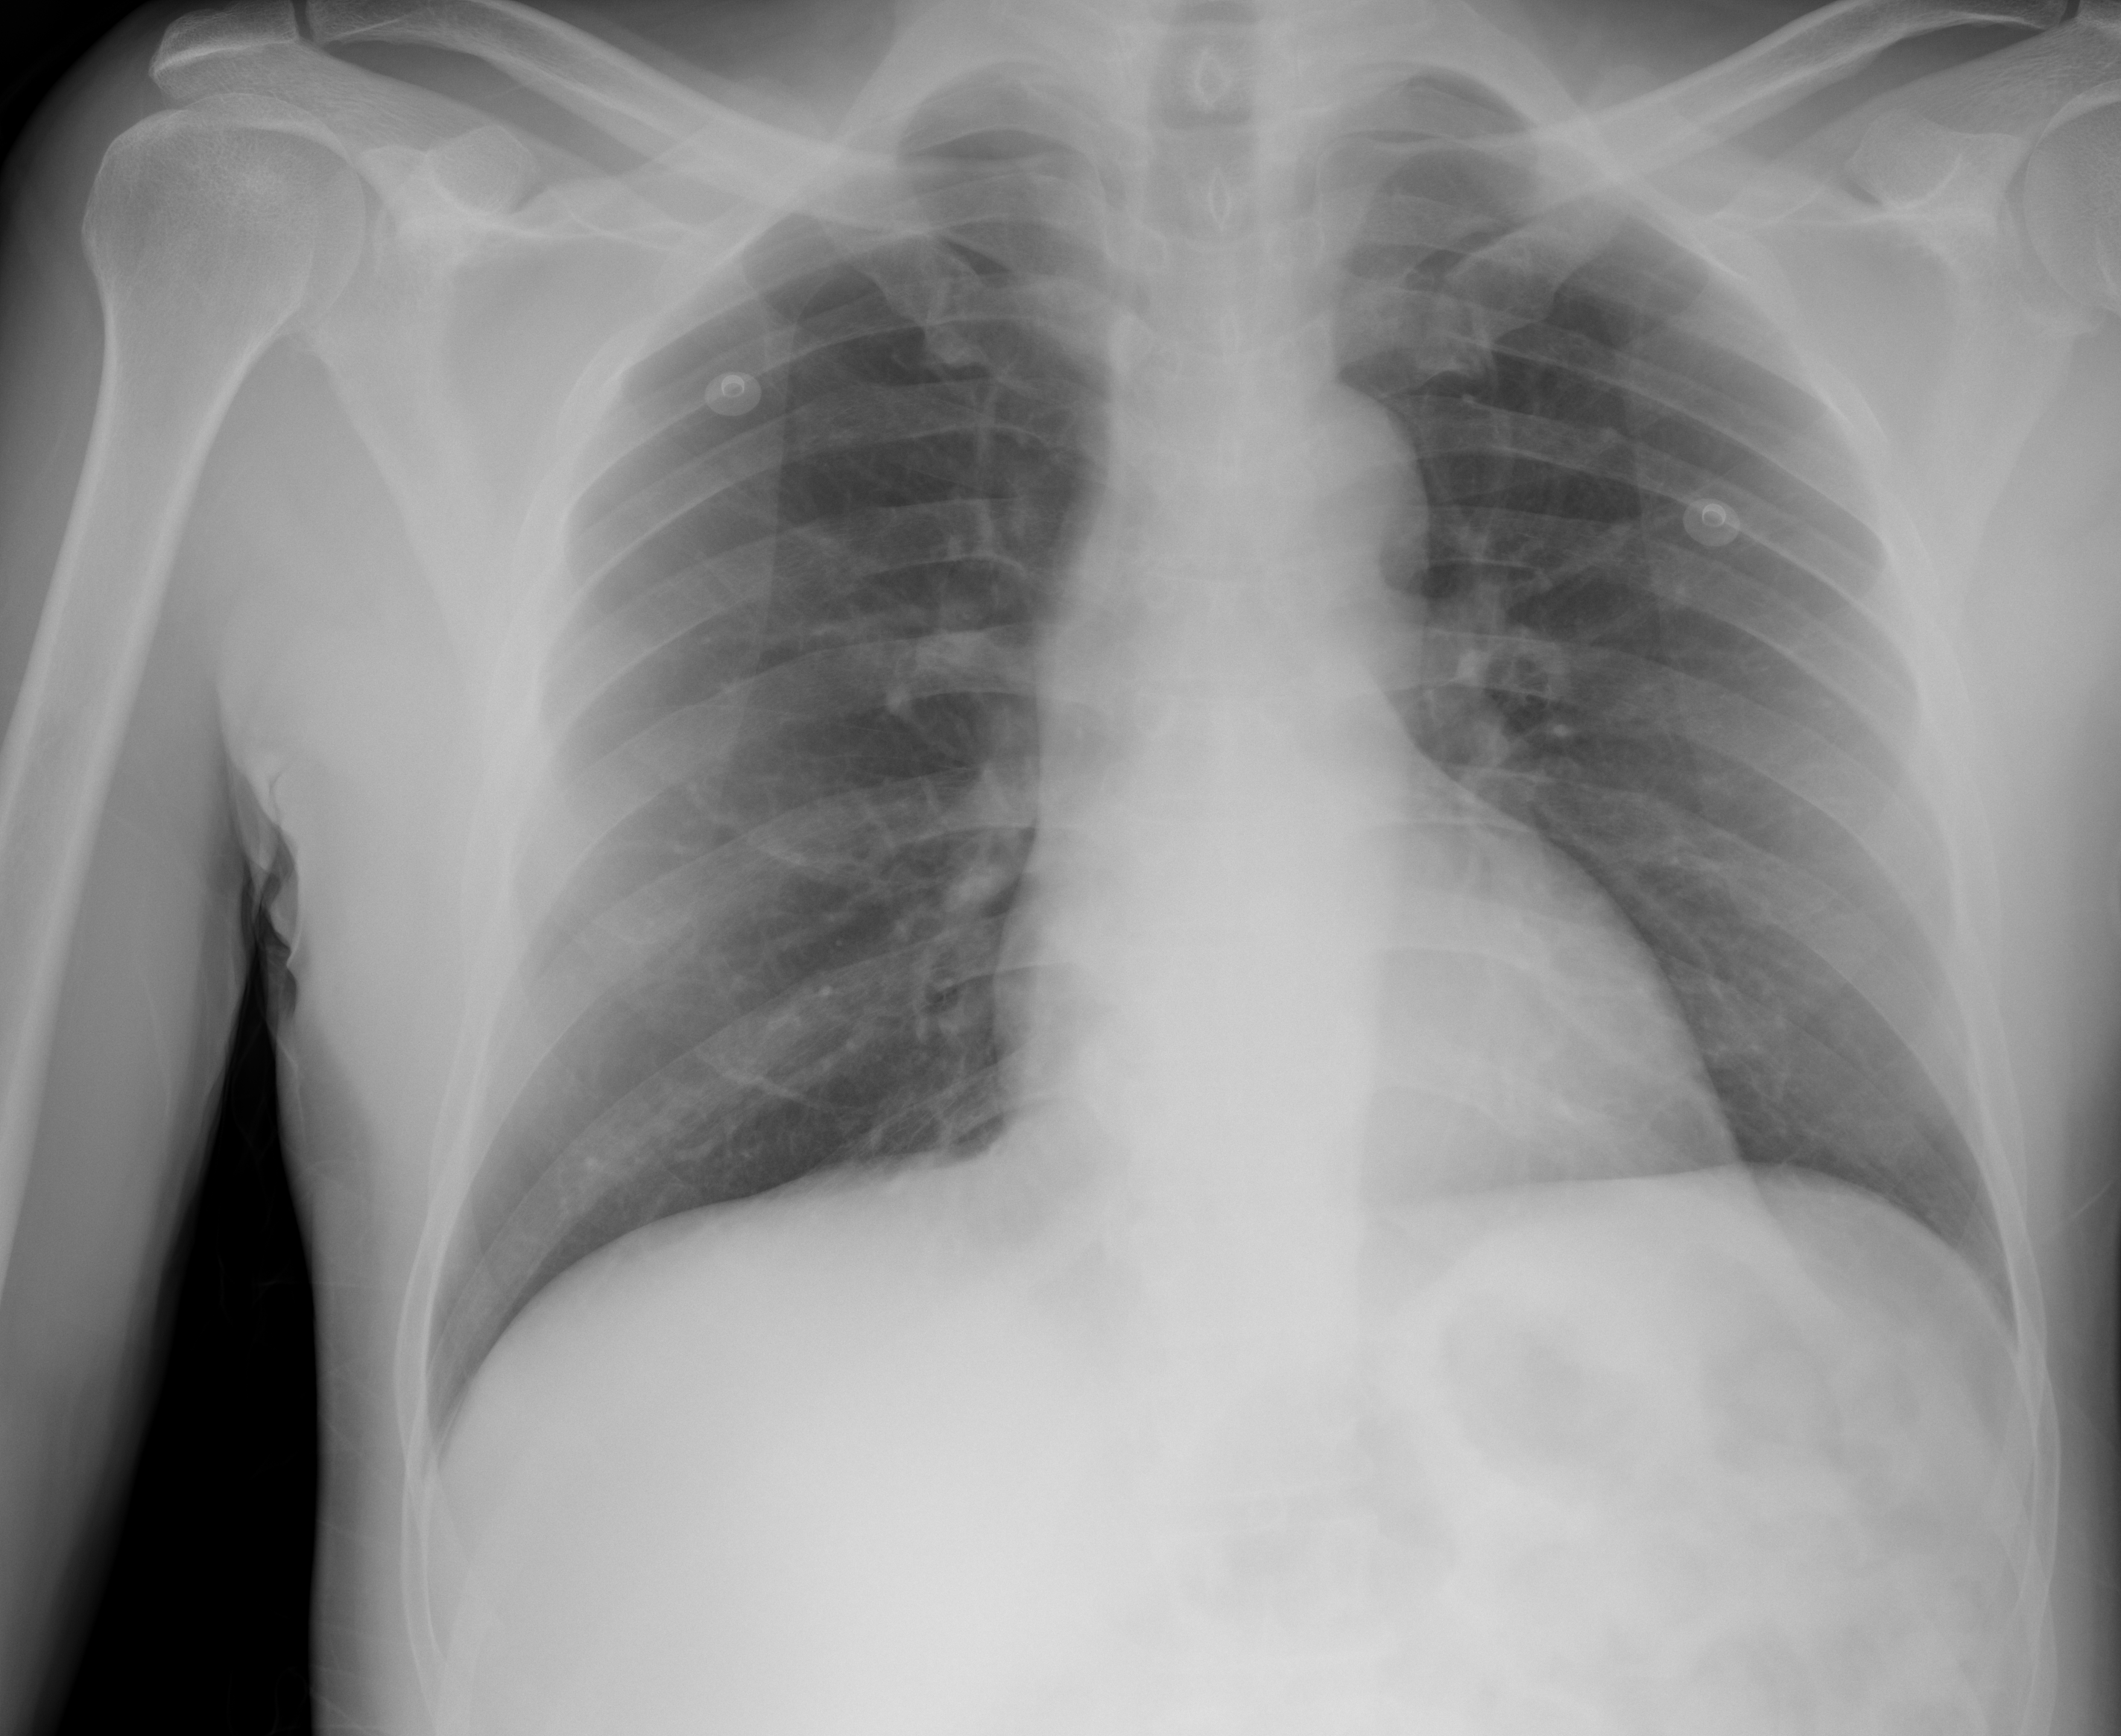
Portable chest radiograph, AP projection. Male patient, age 60 years; imaged 0 days after the COVID-19 diagnosis.
Radiologist's key findings for this exam: lungs are clear, with no focal airspace disease.